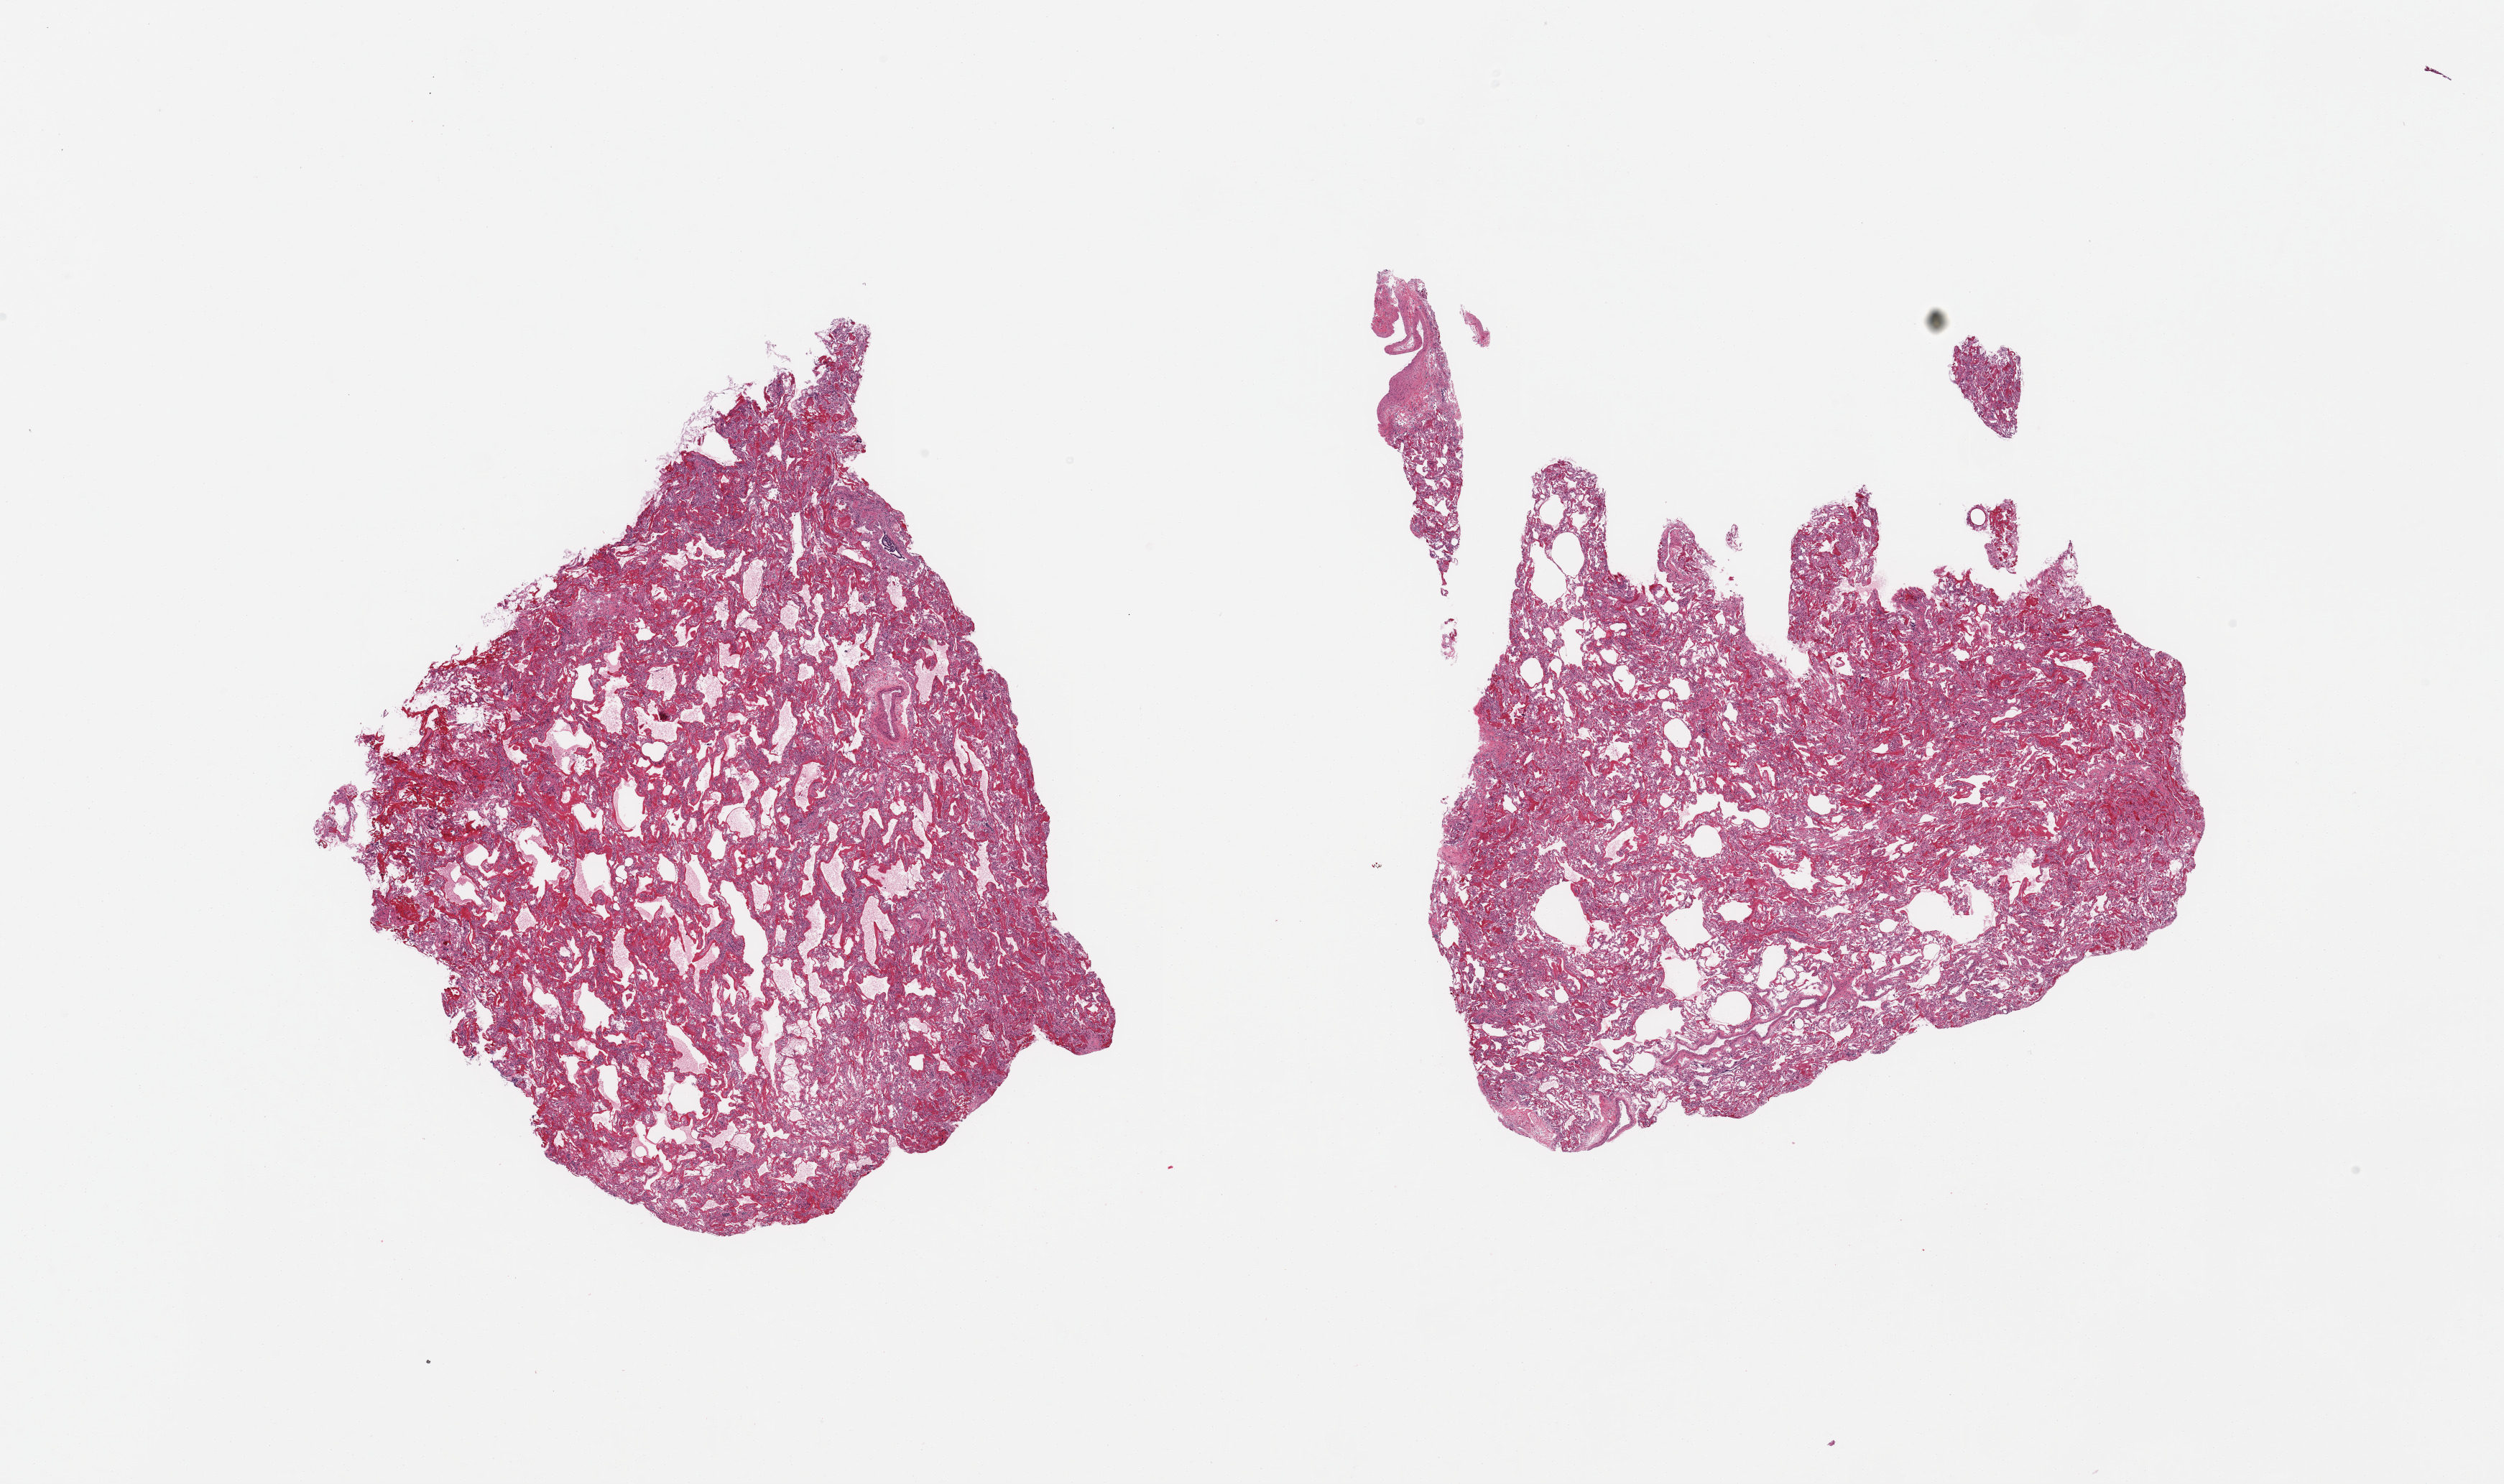
Whole-slide image, hematoxylin and eosin (H&E) stain, brightfield, whole scanned area (about 27.6 x 16.3 mm, from a 20x scan) shown as a low-resolution overview. PAXgene-fixed, paraffin-embedded tissue. Section of lung (target tissue). Tissue donor sample. Donor: female.
• reviewer comment on this tissue sample: 2 pieces; organizing pneumonia